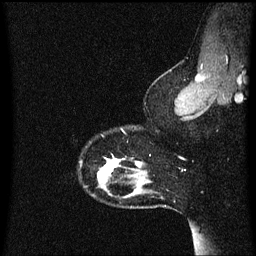
Breast MRI (dynamic contrast-enhanced), one sagittal slice. Slice 52 of 60 in the series (ordered by position). Dynamic contrast-enhanced series, image 2 of 3 at this slice position (ordered by acquisition). 1.5 T. TE 4.2 ms, TR 8.4 ms. 2 mm slice thickness. 256 × 256 image matrix, field of view 200 × 200 mm. Female patient, age 33 years.
Annotated regions visible in this slice (semi-automatic segmentation, software-assisted and operator-edited):
- analysis volume of interest (the breast-tissue region the enhancement analysis was run in; not a lesion): box from (x=81, y=146) to (x=152, y=191) px
- tumour enhancement mask (voxels above the 70 % enhancement threshold inside the analysis volume of interest): (x=98, y=154)–(x=142, y=179)